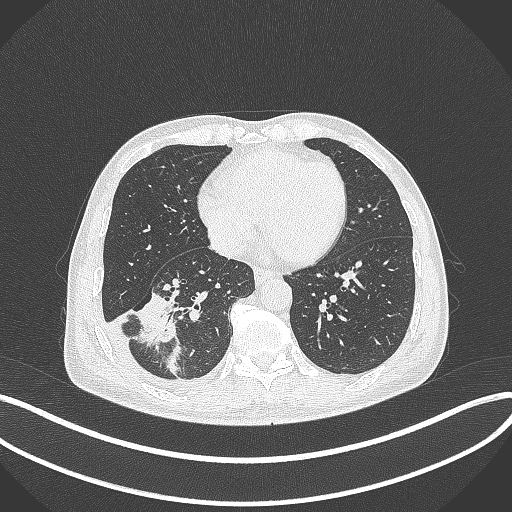
Chest CT, one axial slice; position 135 of 388 along the scan axis; reconstruction kernel B70f; lung window (W 1500 / L -600 HU); 1 mm slice thickness; 512 × 512 image matrix, field of view 400 × 400 mm. Patient: male, 64 years. Case-level facts recorded for this patient, not image findings: clinical TNM (as recorded): T3 N0 M0.
Structures marked on this image (rectangle marked by the reading radiologist):
- lung tumour (recorded histology: adenocarcinoma): box from (x=128, y=283) to (x=184, y=351) px